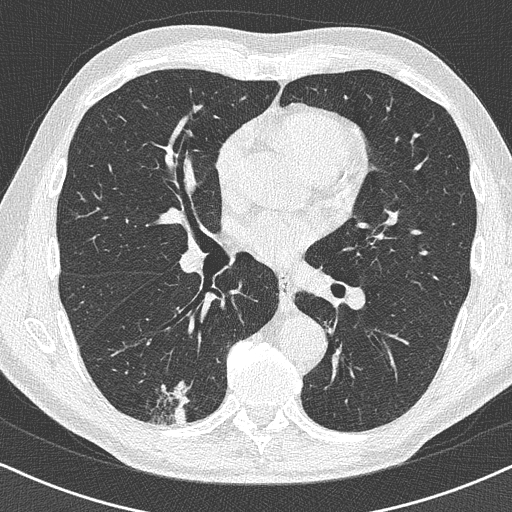
Axial slice from a low-dose chest CT screening exam. Baseline annual screen. Lung window (W 1500 / L -600 HU). 1 mm slice thickness. 512 × 512 image matrix, field of view 320 × 320 mm. Male participant, aged 63 years at enrolment. Former smoker at enrolment.
Lesion marked by an expert reader, bounding box (x1, y1, x2, y2) in pixels: (135, 369, 206, 430). Screening reader's record for this exam (one nodule recorded; not confirmed to be the boxed lesion): non-calcified nodule or mass ≥4 mm, right lower lobe, 16 × 13 mm, poorly defined margins.